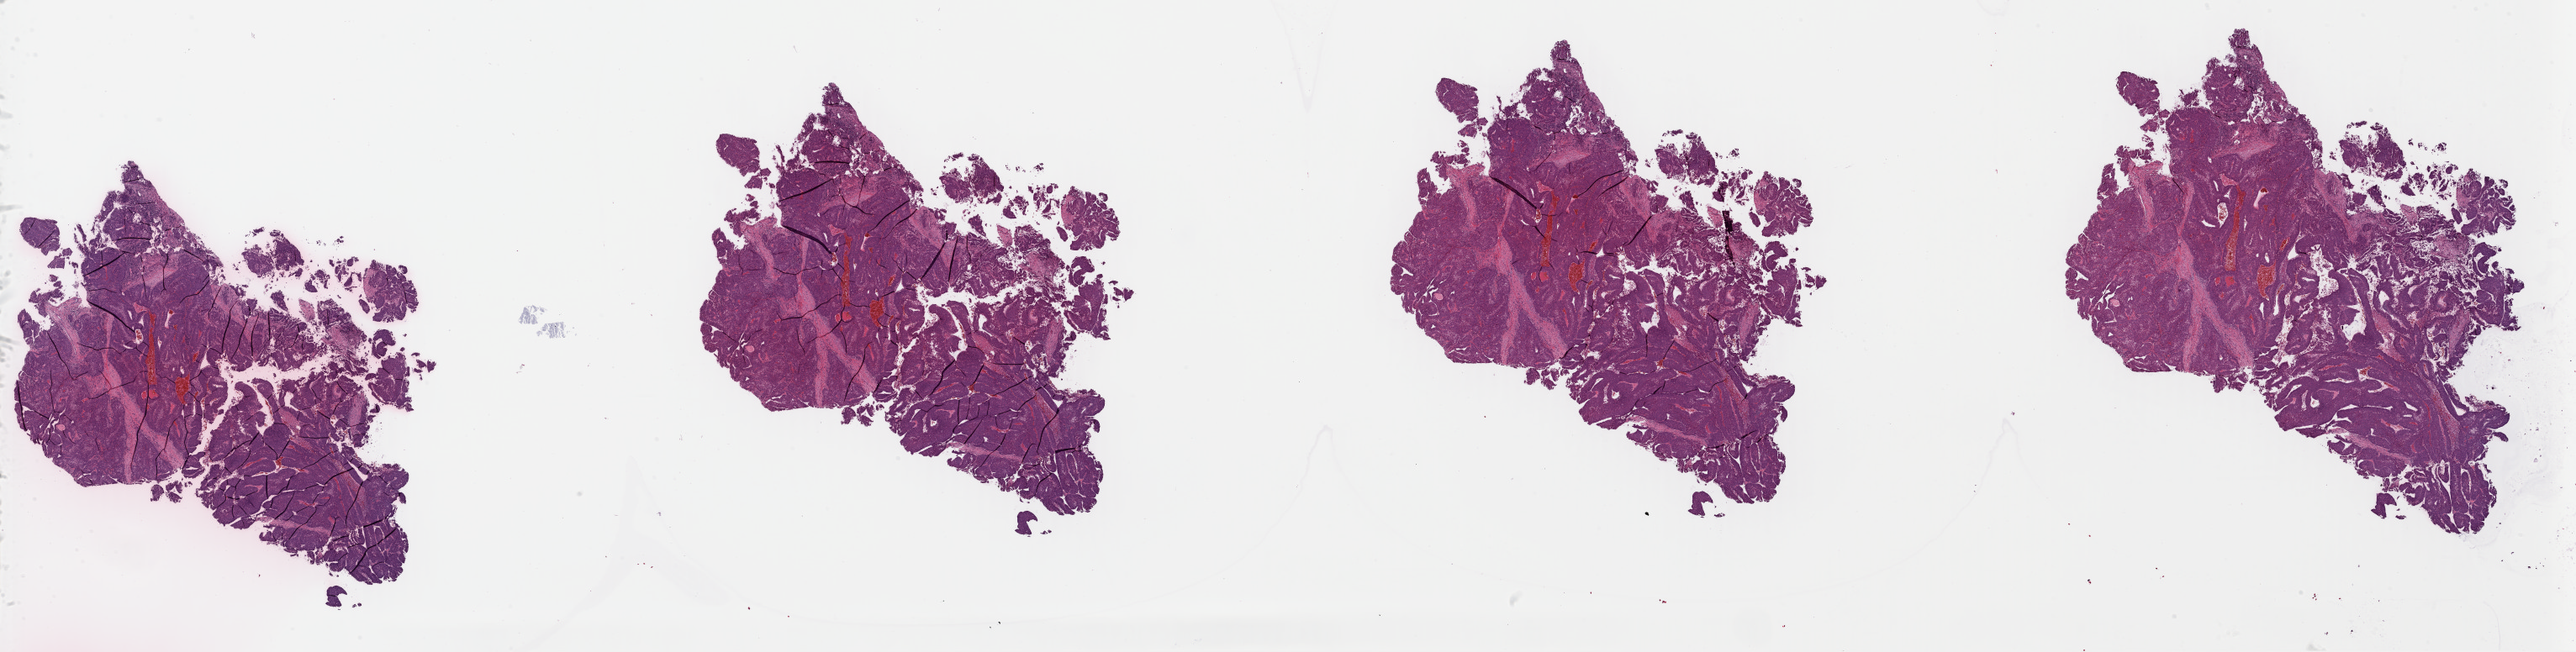
Whole-slide histology image, H&E, low-resolution overview of the scanned area, about 48.2 x 12.2 mm; FFPE section; liver, primary tumour sample. Female patient; age at initial diagnosis 52 years. Histologic grade: G3 (poorly differentiated).
AJCC pathologic stage: IIIA. Diagnosis: Hepatocellular carcinoma, NOS. TNM: T3a NX MX.